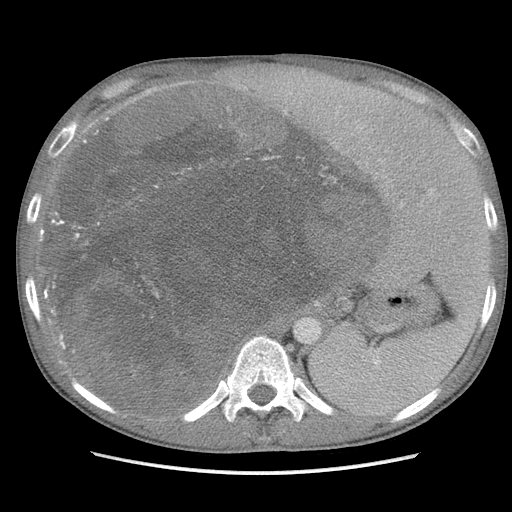
Contrast-enhanced abdominal CT, one axial slice. Slice 77 of 115 in the series (ordered by position). Soft-tissue window (W 400 / L 40 HU). 5 mm slice thickness. 512 × 512 image matrix, field of view 360 × 360 mm. Male patient. Case-level facts recorded for this patient, not image findings: diagnosis: adrenocortical carcinoma; tumour side: right adrenal; Ki-67 index: 13 %; stage (as recorded): 3.
Structures marked on this image (semi-automatic segmentation, software-assisted and operator-edited):
- mass: bounding box (x1, y1, x2, y2) in pixels: (51, 88, 377, 412)